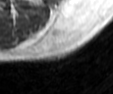
MRI of an extremity soft-tissue mass, one axial slice. Position 34 of 42 along the scan axis. MR volume resampled by the dataset authors to the PET/CT grid (not the native acquisition matrix). 3.27 mm slice thickness. 113 × 94 image matrix, field of view 110 × 92 mm. Male patient. From the clinical record (not read from this slice): histological type: leiomyosarcoma; grade: intermediate; site of the primary tumour: left pelvis.
Annotated regions visible in this slice (expert contour drawn on MRI and transferred to this co-registered scan by the dataset authors):
- gross tumour volume (mass): bounding box [x1, y1, x2, y2] px = [40, 21, 71, 53]